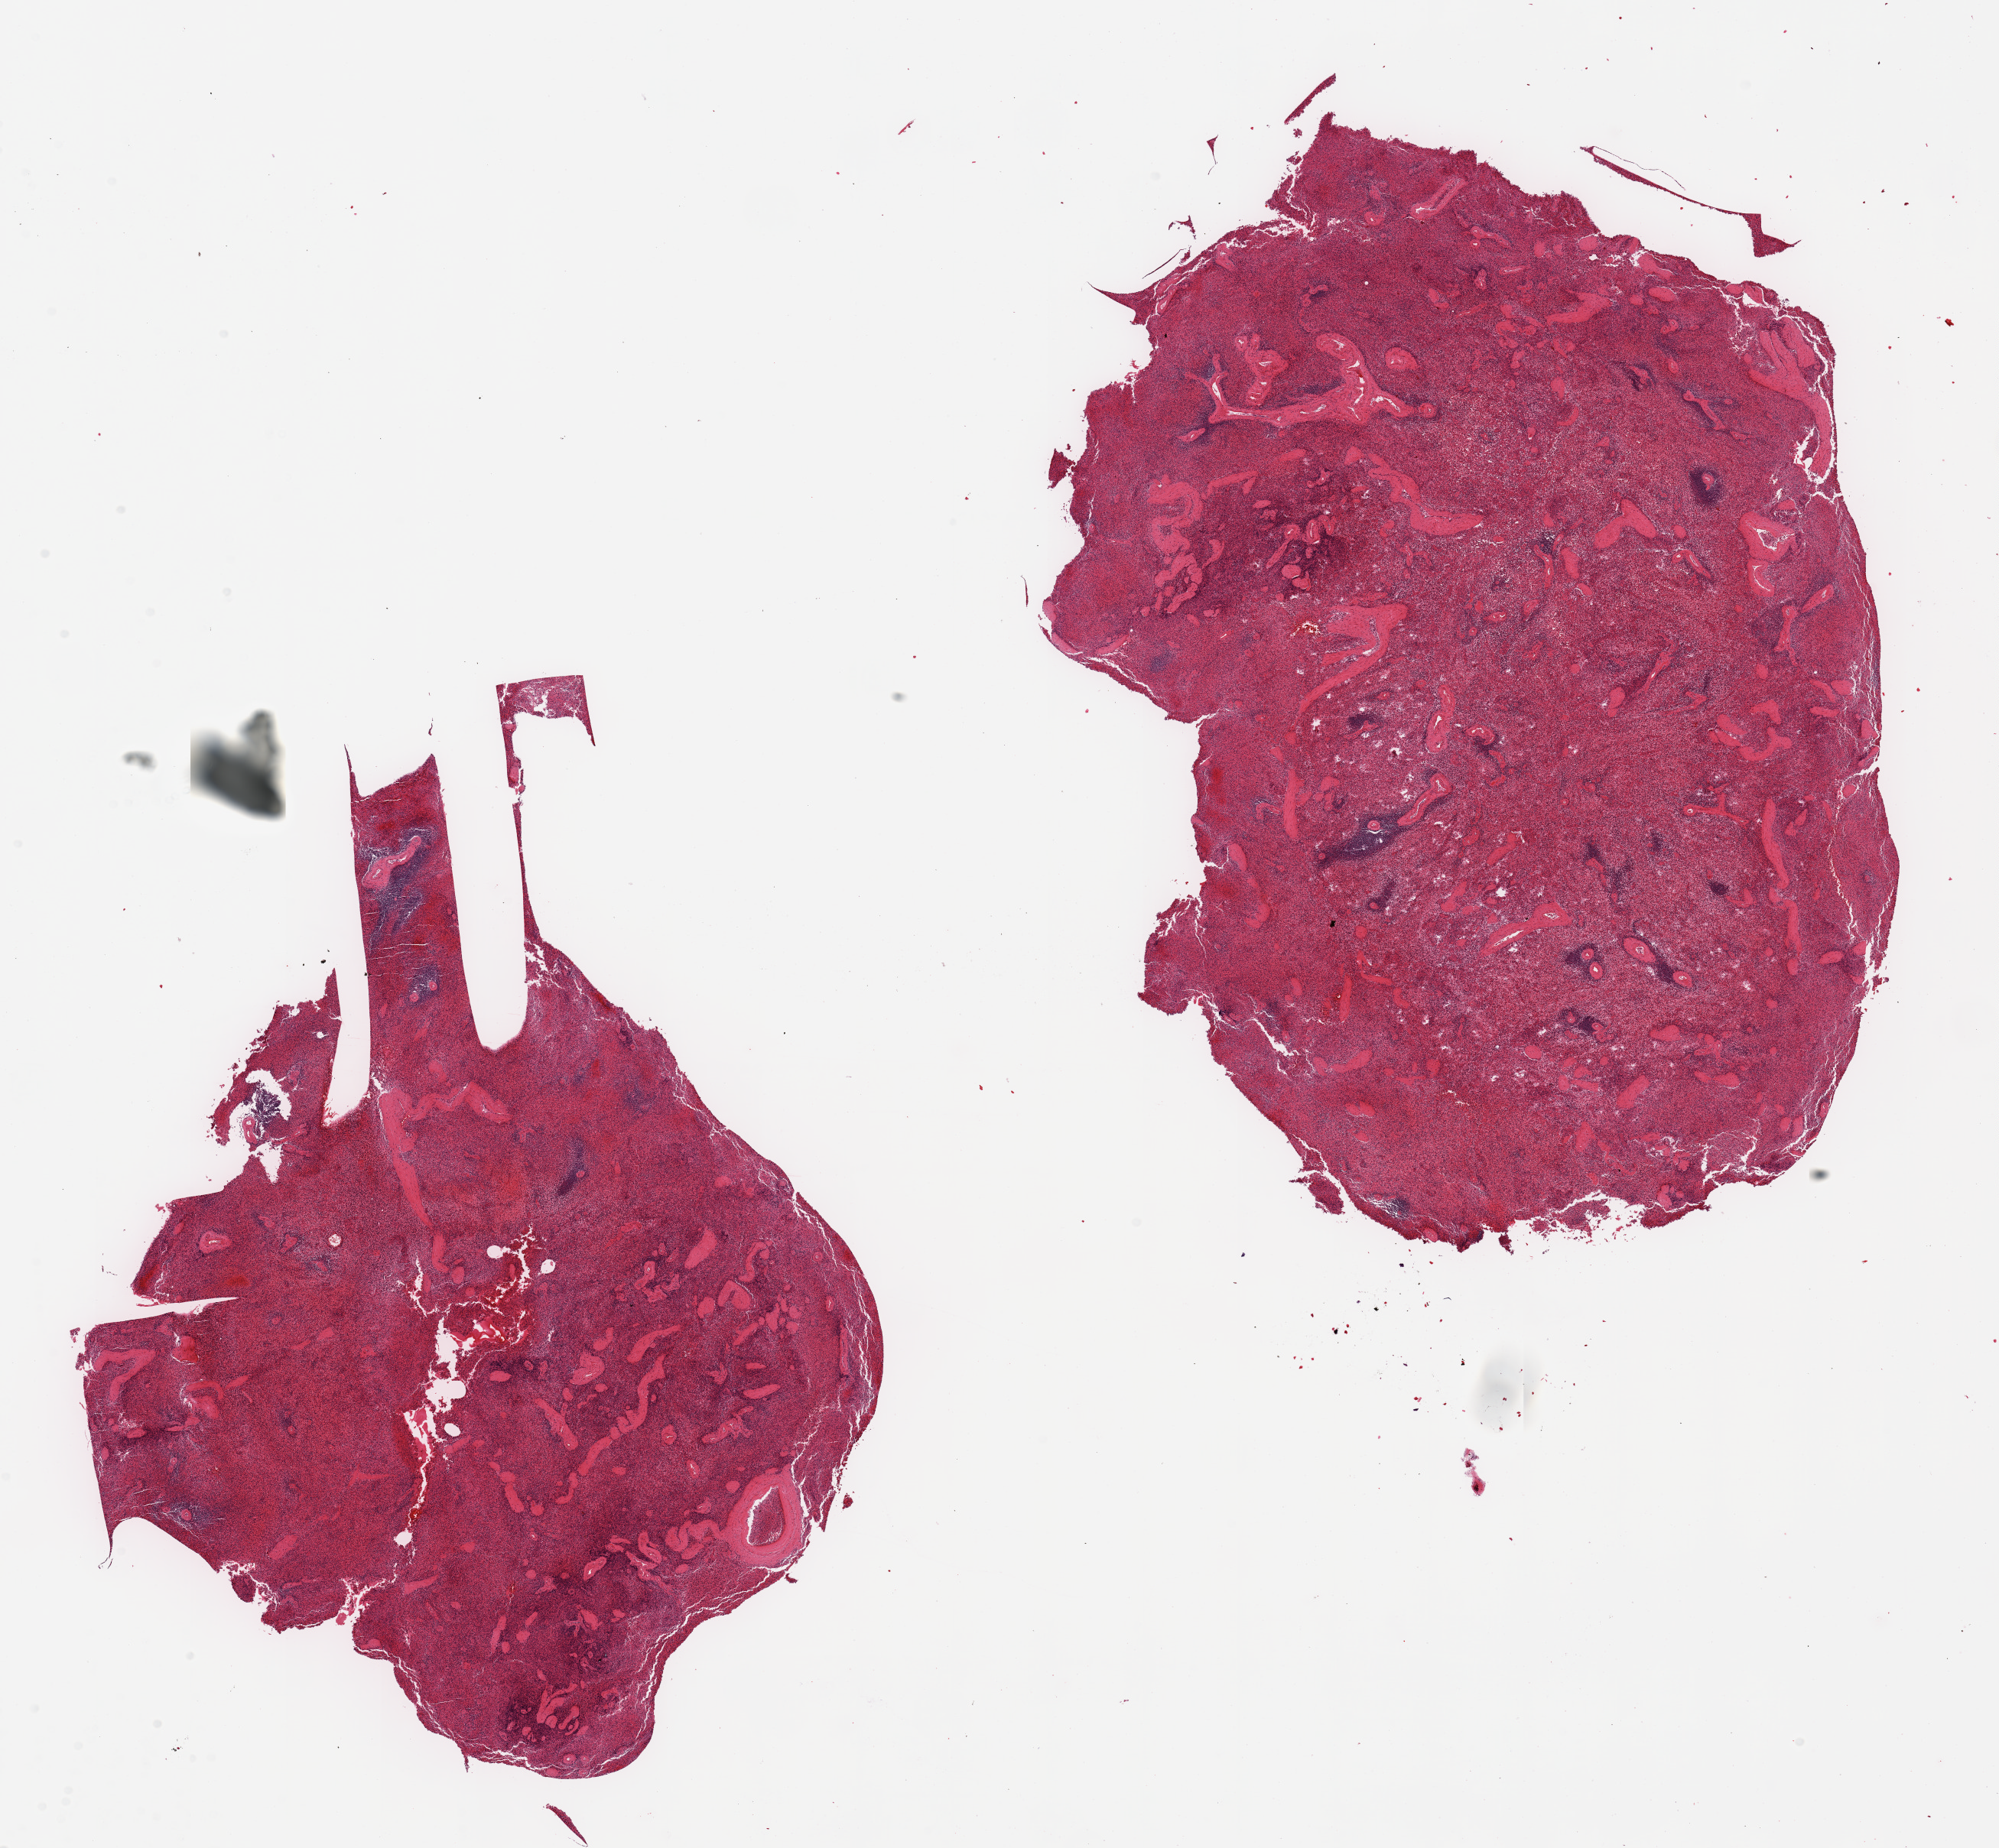
Digitized haematoxylin and eosin-stained section — shown as a low-resolution overview of the whole scanned area (about 20.7 x 19.1 mm, slide scanned at 20x); PAXgene-fixed paraffin-embedded (PFPE) section; section of spleen (target tissue); donor tissue sample. Male donor.
Reviewer comment on this tissue sample: 2 pieces; marked congestion.